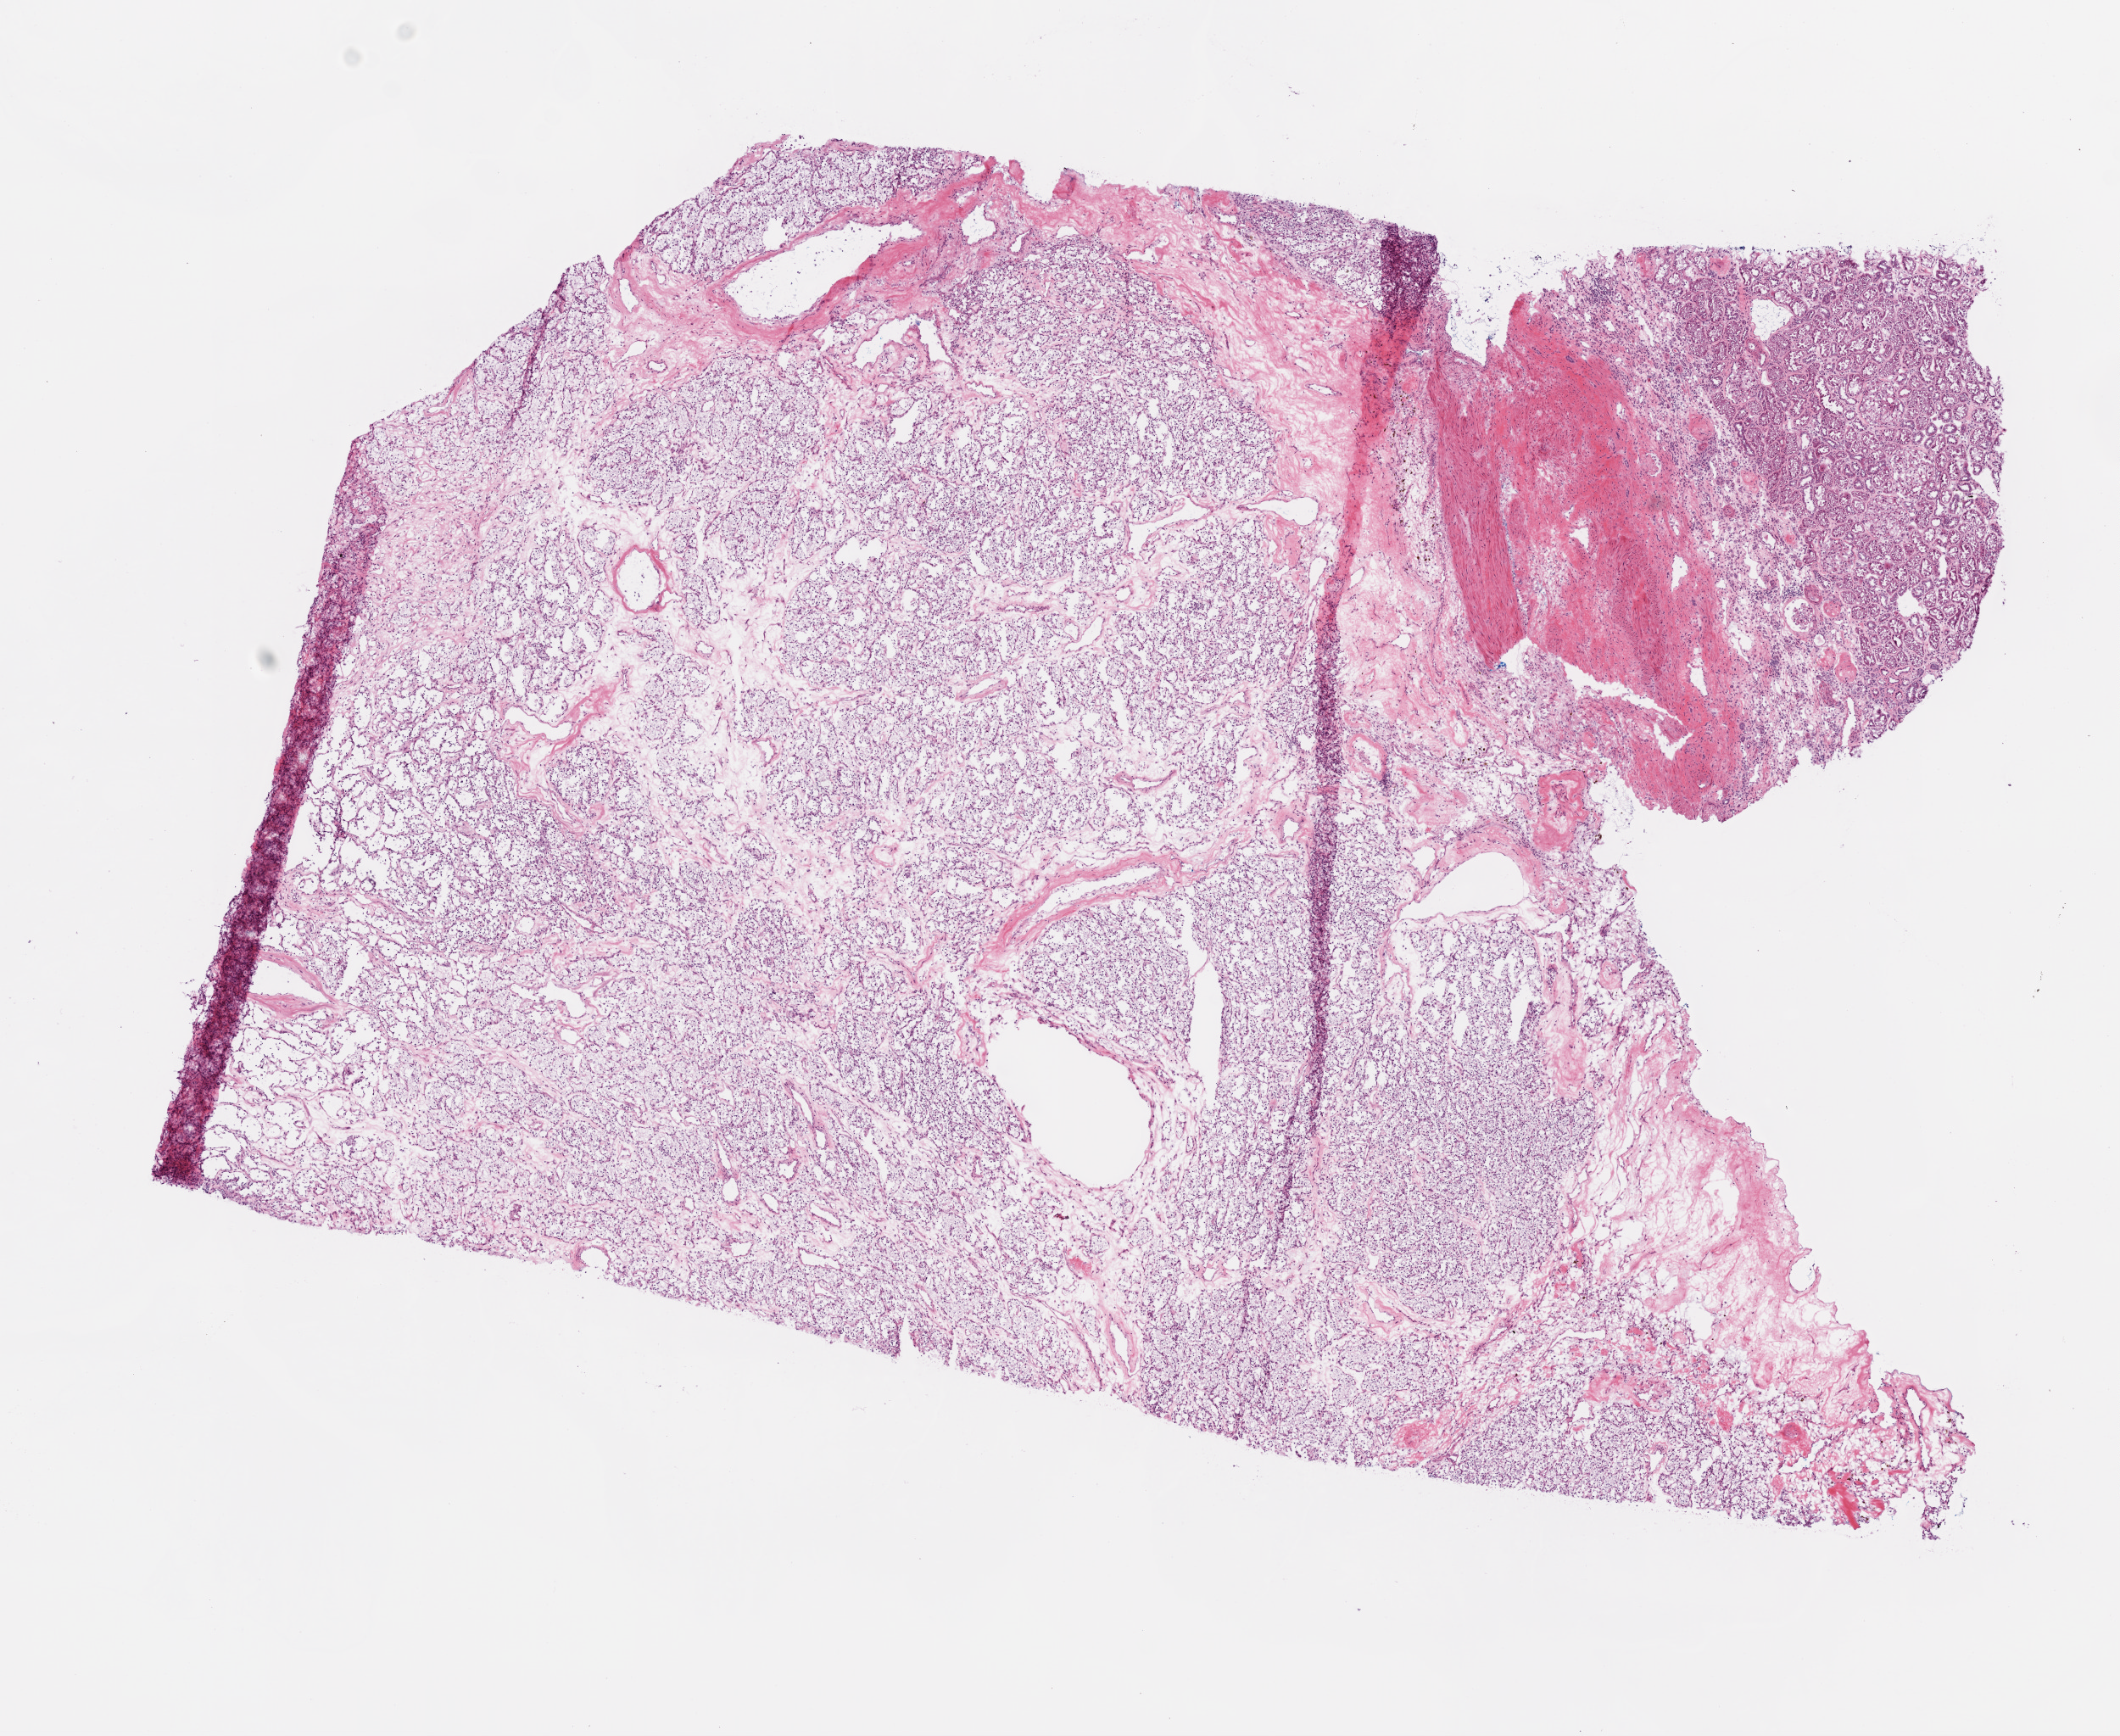
H&E whole-slide image, a low-resolution overview of the entire scanned area, about 10.0 x 8.2 mm (acquisition: 20x scan). Frozen section from the top of the tissue portion. Kidney, primary tumour sample. Patient: male, age at initial diagnosis 43 years. Histologic grade: G2 (moderately differentiated). Slide review estimates, as recorded: tumour cells 75%, tumour nuclei 80%, normal cells 15%, stromal cells 10%, necrosis 0%.
Diagnosis: Clear cell adenocarcinoma, NOS. AJCC pathologic stage: I (7th edition). TNM: T1a N0 M0.